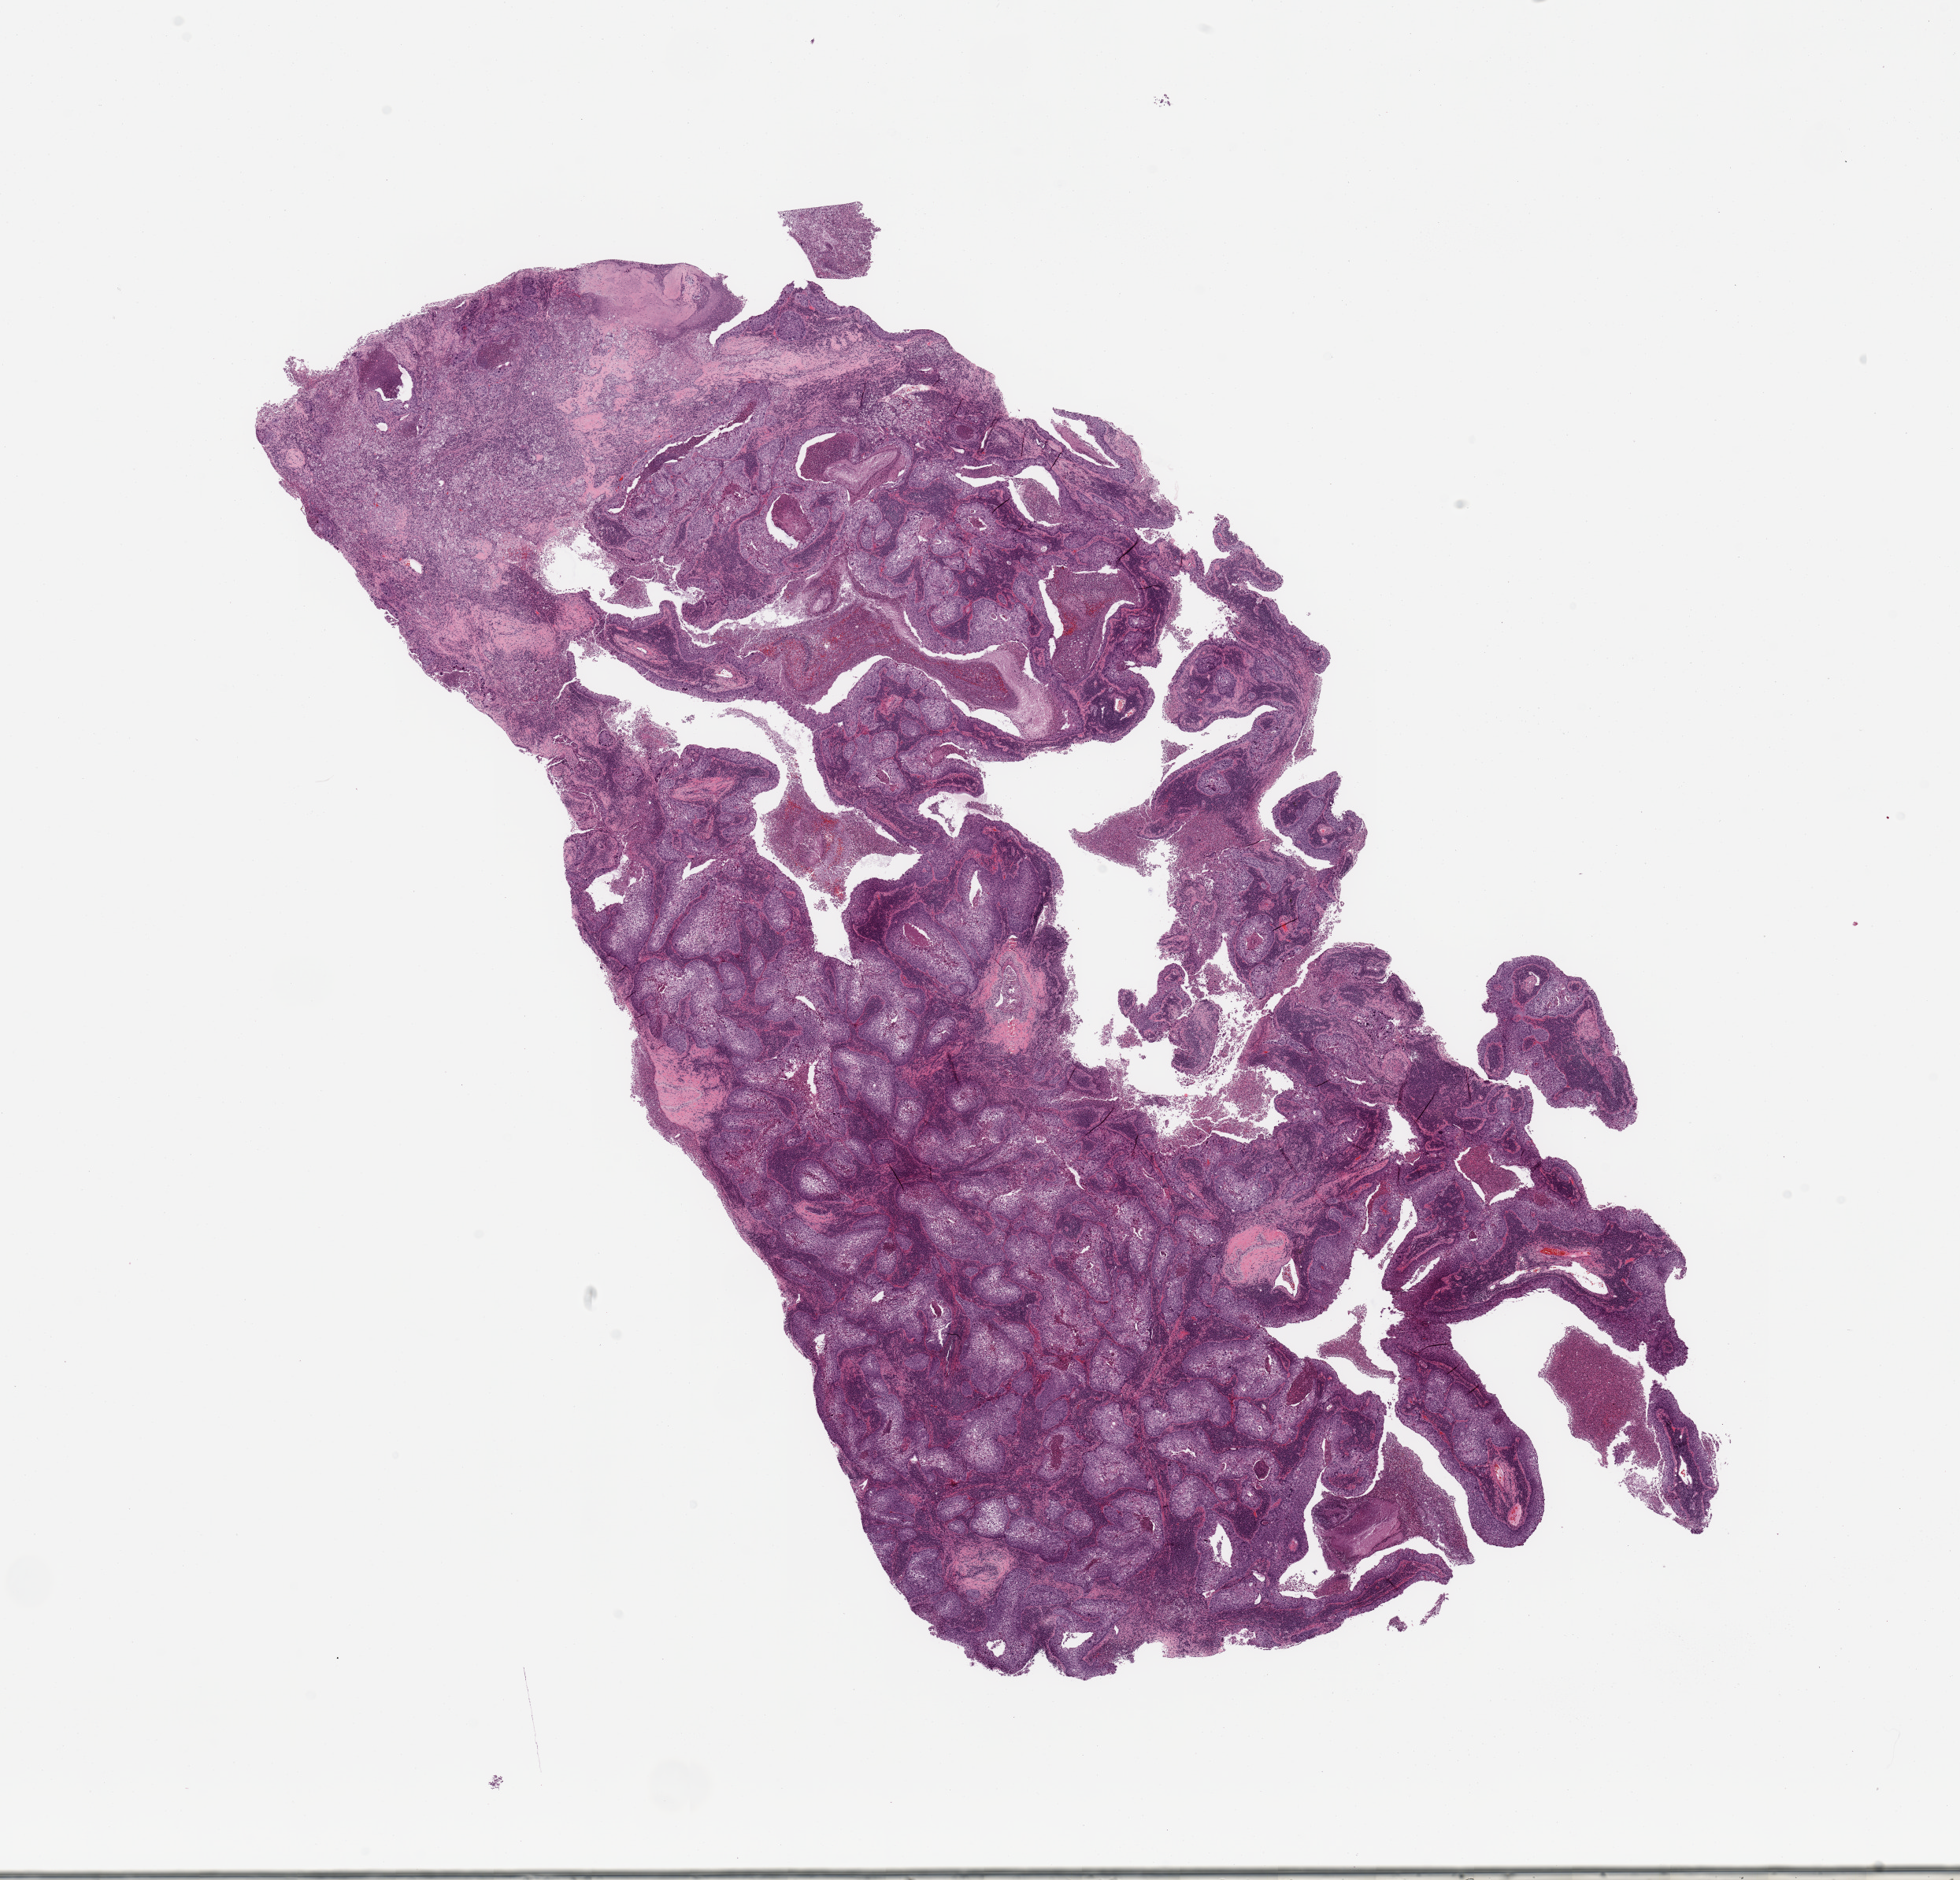
Whole-slide histology image, H&E, whole scanned area (about 19.7 x 18.9 mm, from a 20x scan) shown as a low-resolution overview, tumour tissue sample, sampled site: lung. Female, 64 y/o. Histologic grade: G3 (poorly differentiated). Pathologist review of this section (percent, as recorded): tumour nuclei 65%, necrosis 15%.
- diagnosis: Squamous cell carcinoma, NOS
- AJCC pathologic stage: IIA
- primary tumour site (as recorded): left lower lobe